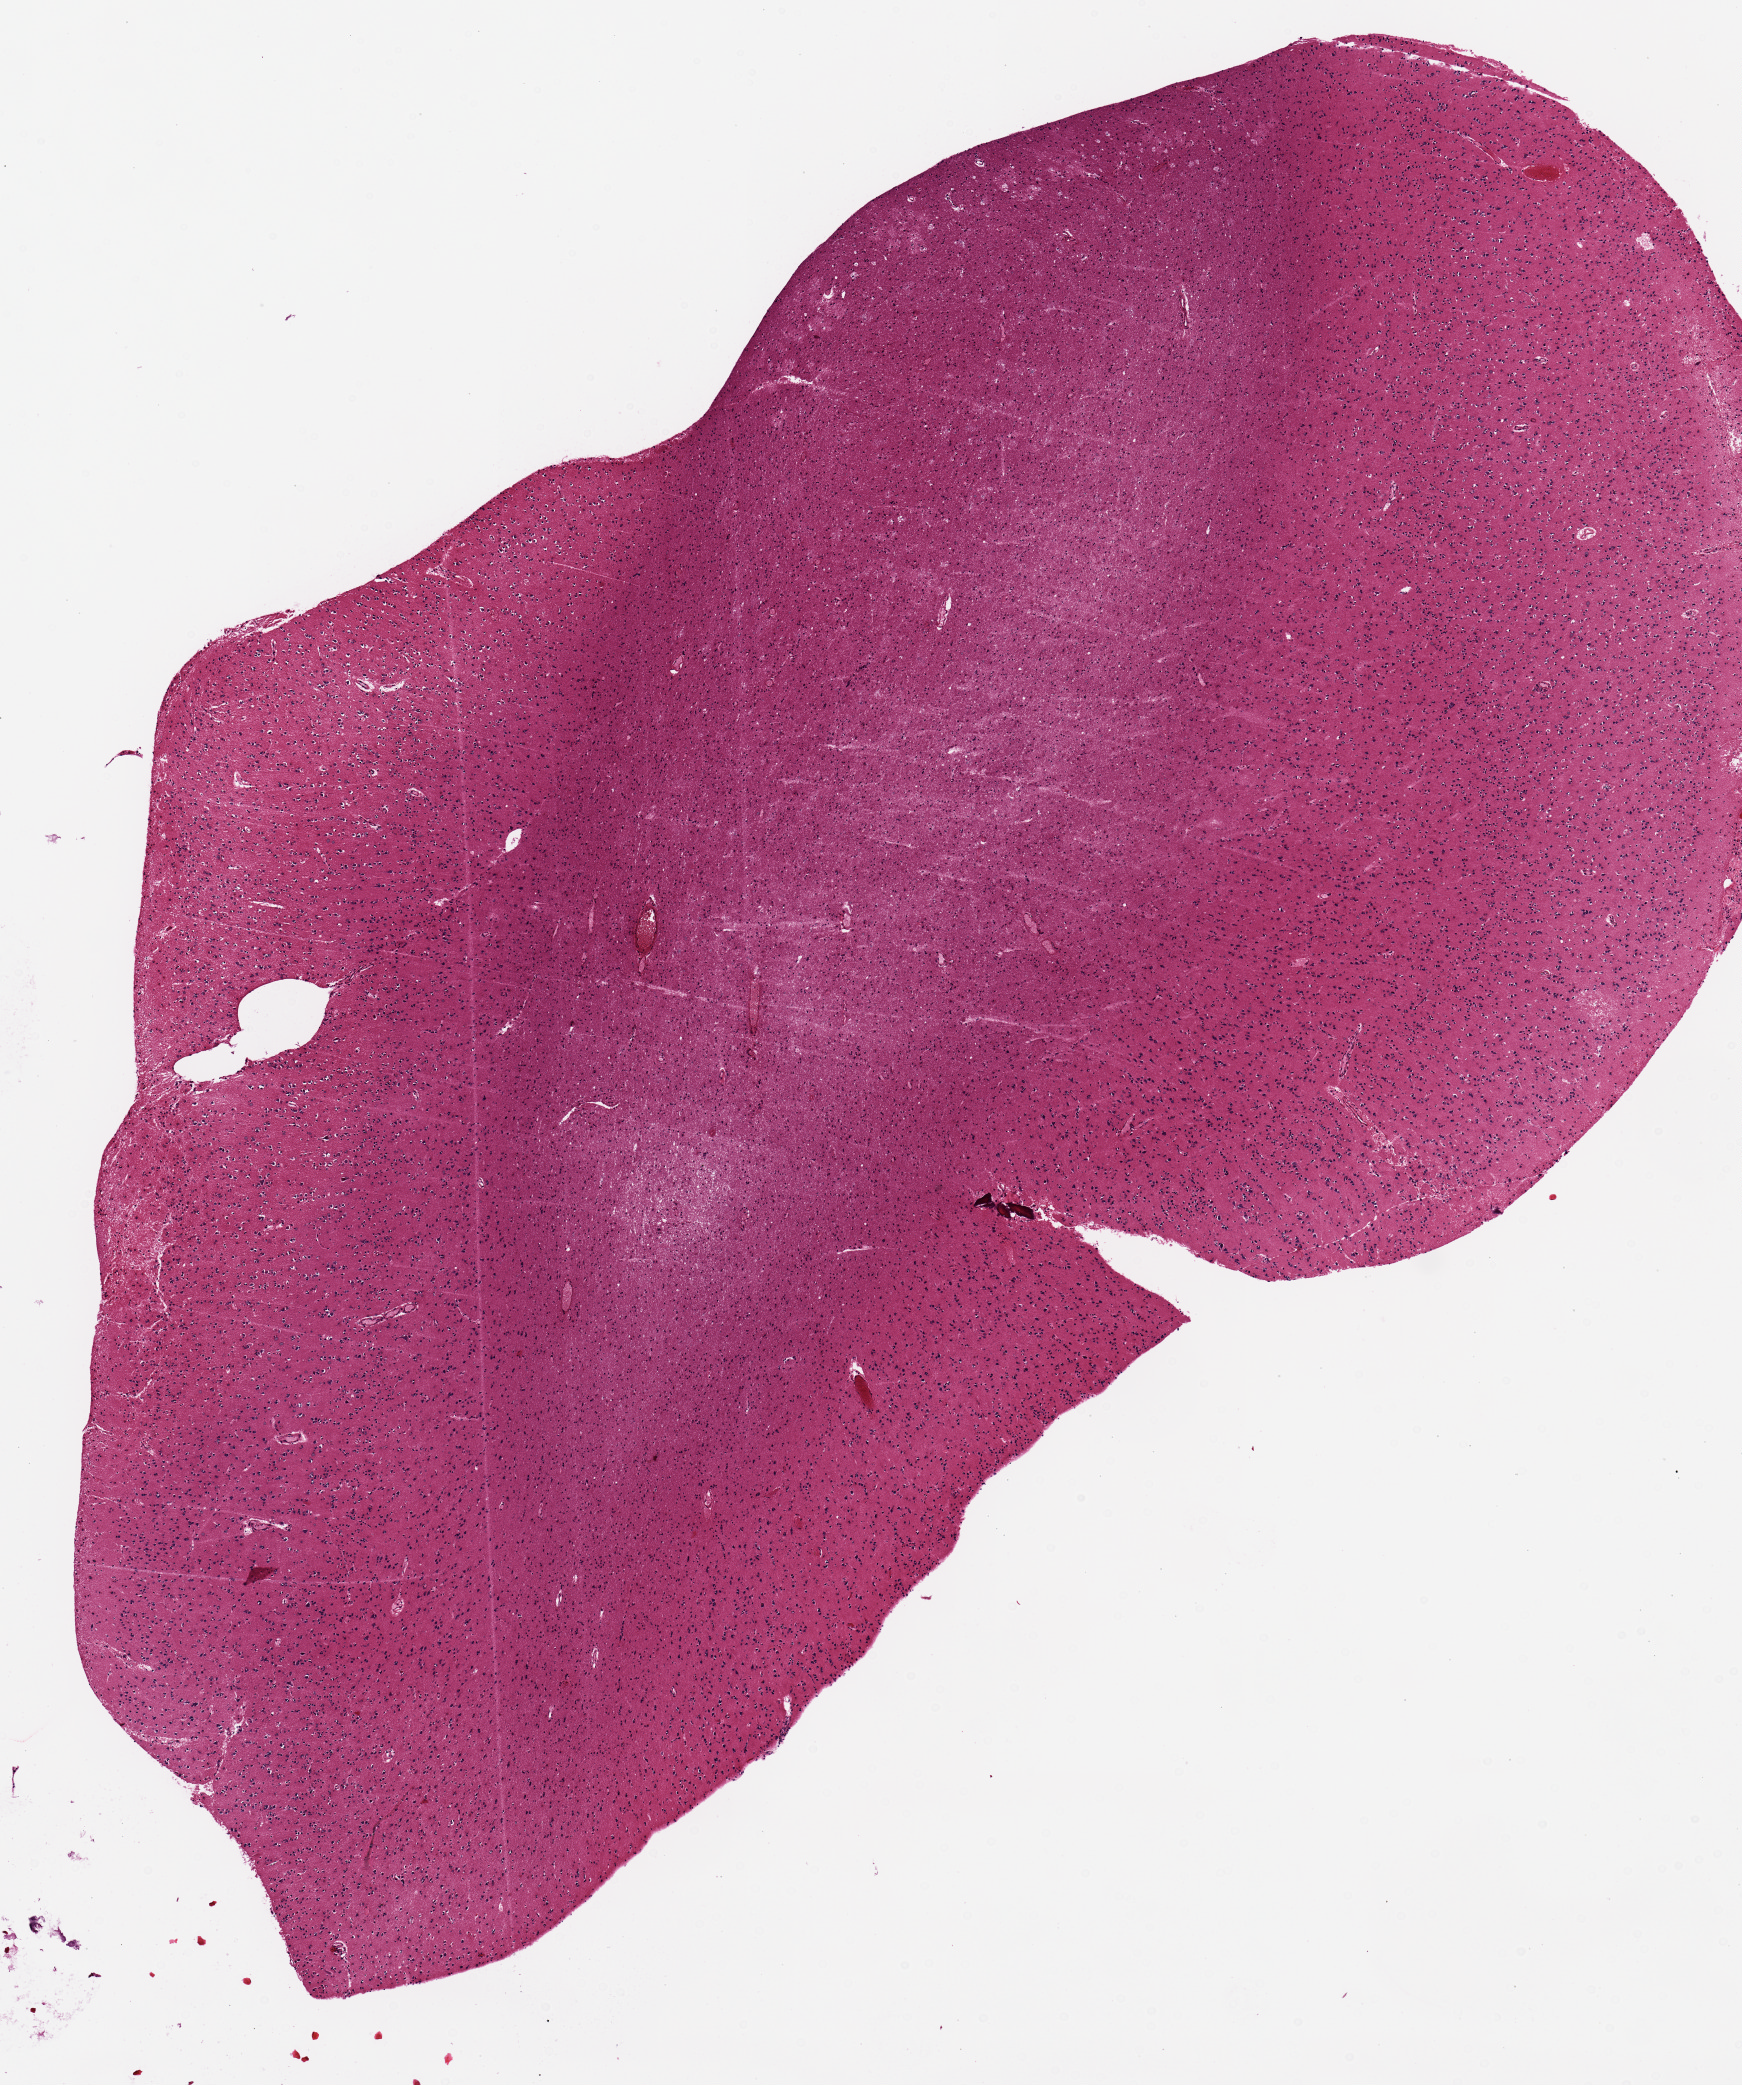
Digitized hematoxylin and eosin (H&E)-stained section, brightfield, a low-resolution overview of the entire scanned area, about 6.9 x 8.2 mm (slide scanned at 20x); PAXgene-fixed, paraffin-embedded tissue; section of cerebral cortex (target tissue); tissue donor sample. Male donor.
* review note (as recorded): 1 piece 9x5 mm; cortex and deep white matter